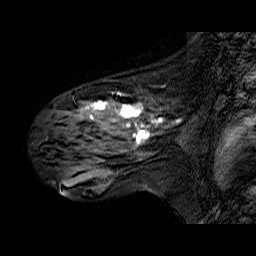
Breast MRI (dynamic contrast-enhanced), one sagittal slice; position 39 of 60 along the scan axis; dynamic contrast-enhanced series, time point 2 of 6 at this slice position (early post-contrast); 1.5 T; TE 6.3 ms, TR 32.9 ms; 4 mm slice thickness; 256 × 256 image matrix, field of view 200 × 200 mm. Female patient. Case-level facts recorded for this patient, not image findings: setting: breast cancer imaged before/during neoadjuvant chemotherapy; receptor status: HER2-positive.
Structures marked on this image (semi-automatic segmentation, software-assisted and operator-edited):
- analysis volume of interest (the breast-tissue region the enhancement analysis was run in; not a lesion): bounding box (x1, y1, x2, y2) in pixels: (33, 90, 174, 173)
- tumour enhancement mask (voxels above the 100 % enhancement threshold inside the analysis volume of interest): (85, 102, 163, 146)